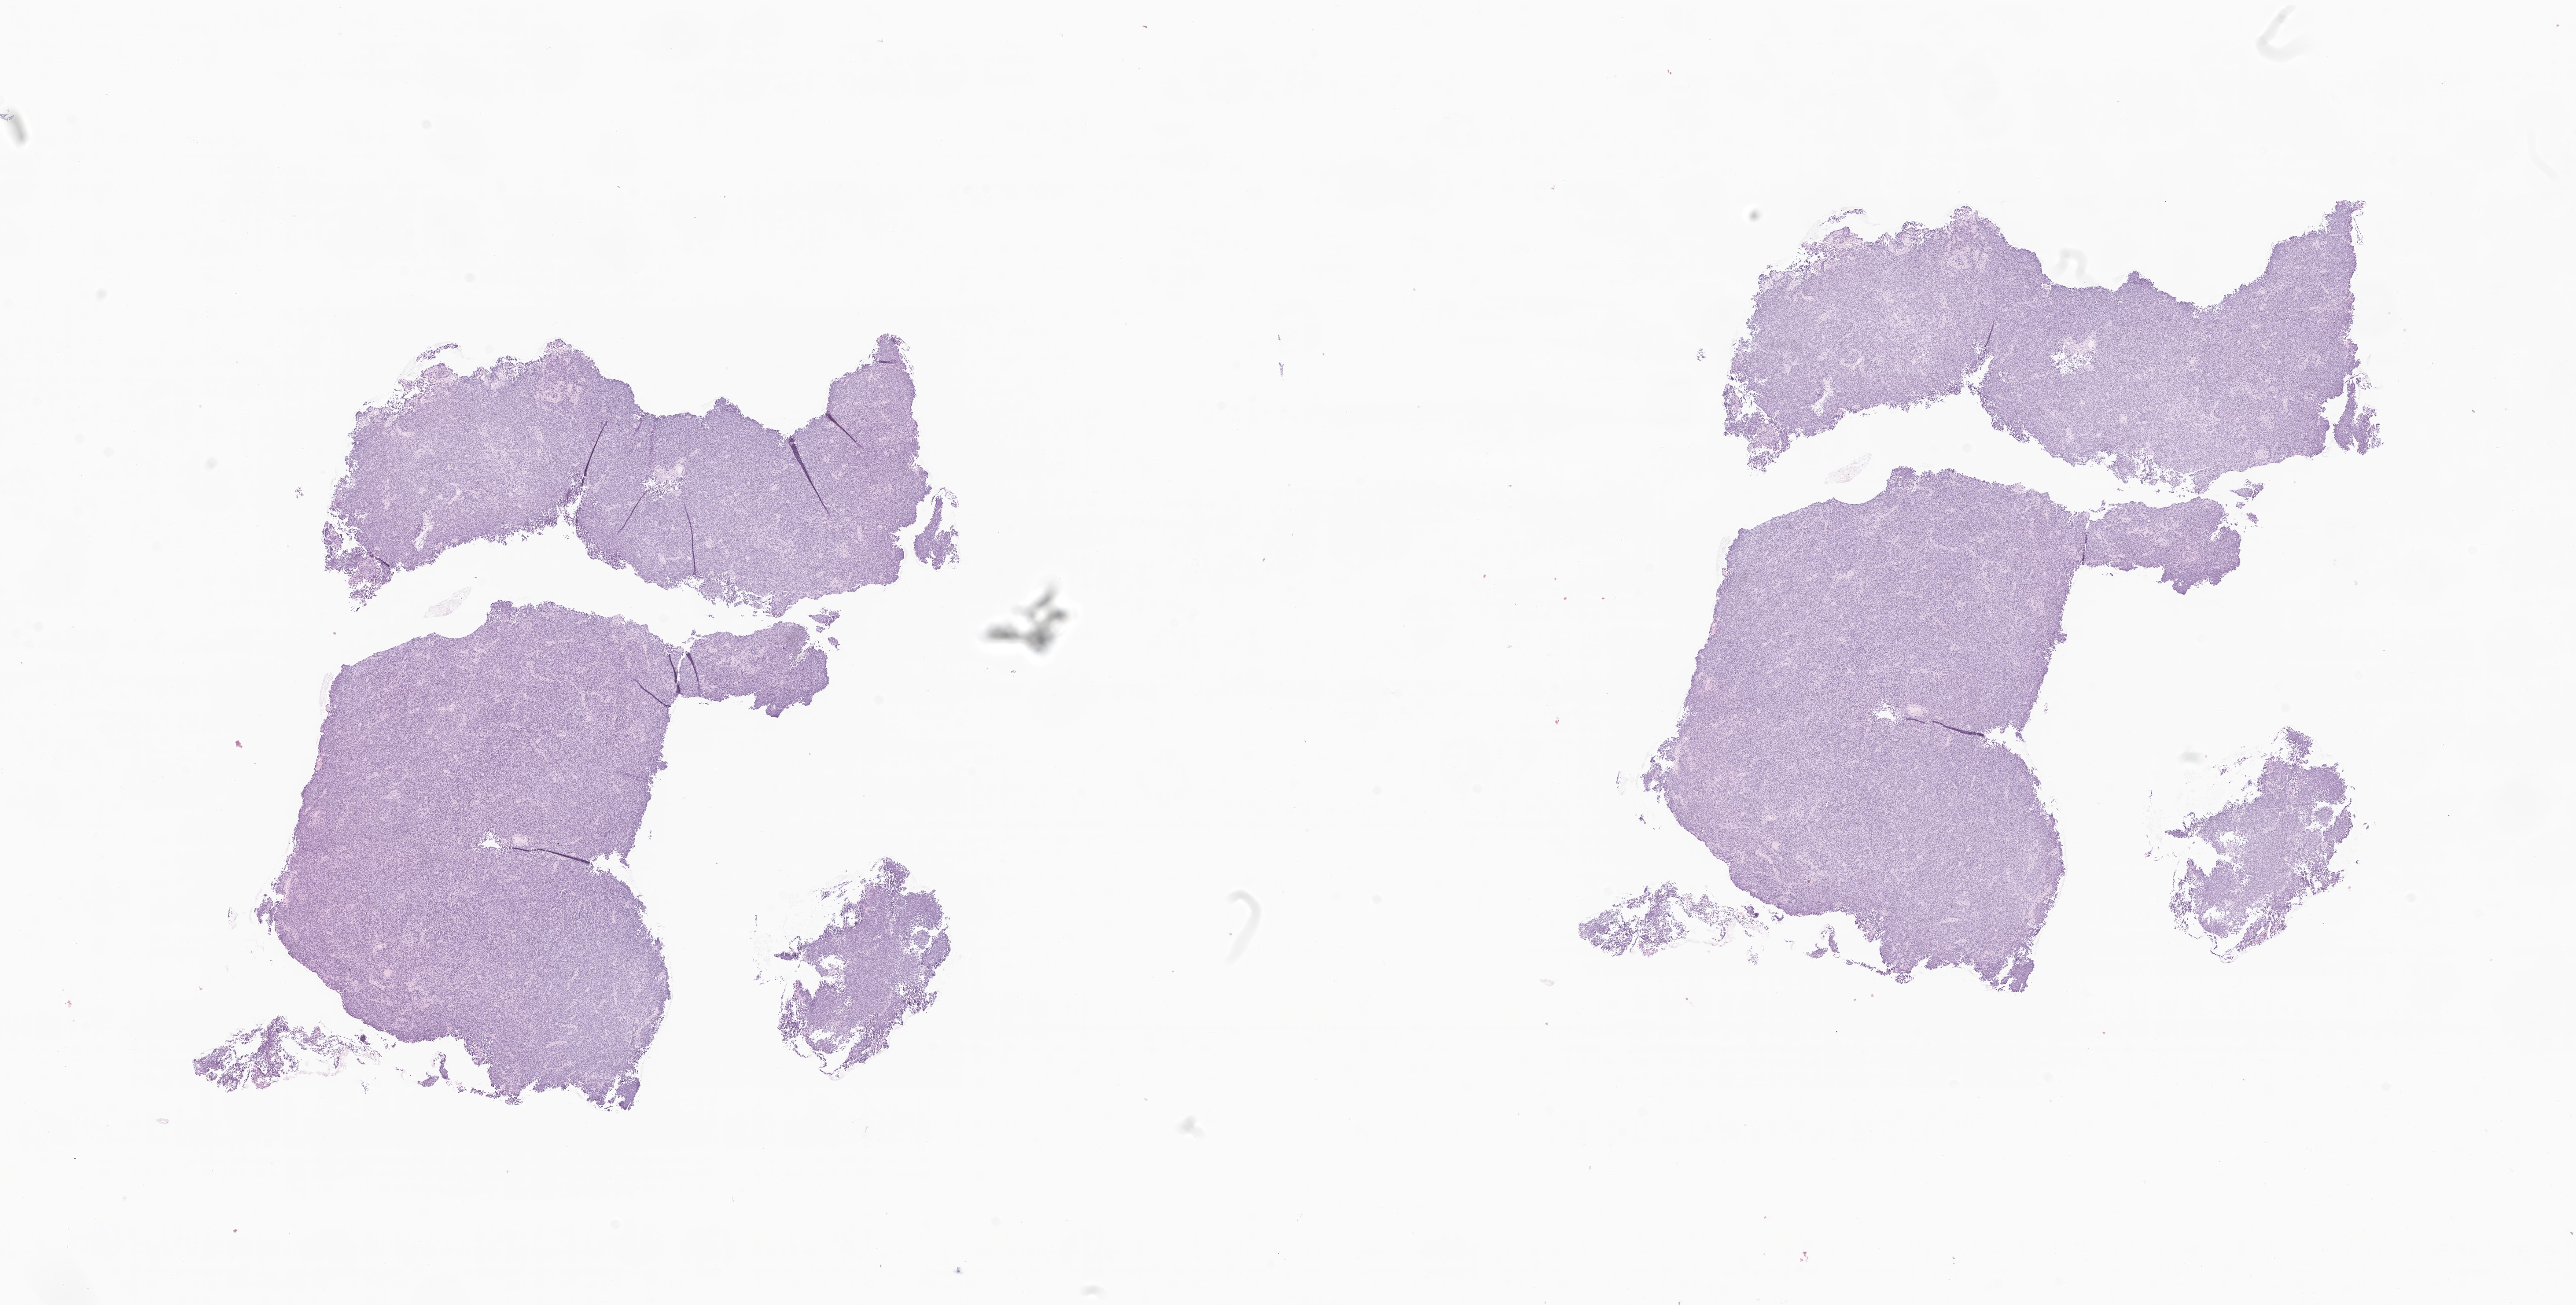
Digitized H&E-stained section of tumor tissue from the brain, shown as a low-resolution overview of the whole scanned area (about 24.7 x 12.5 mm). FFPE section. Patient male; age 57 months (4 years 9 months).
Diagnosis (ICD-O-3 morphology term): Medulloblastoma, NOS.